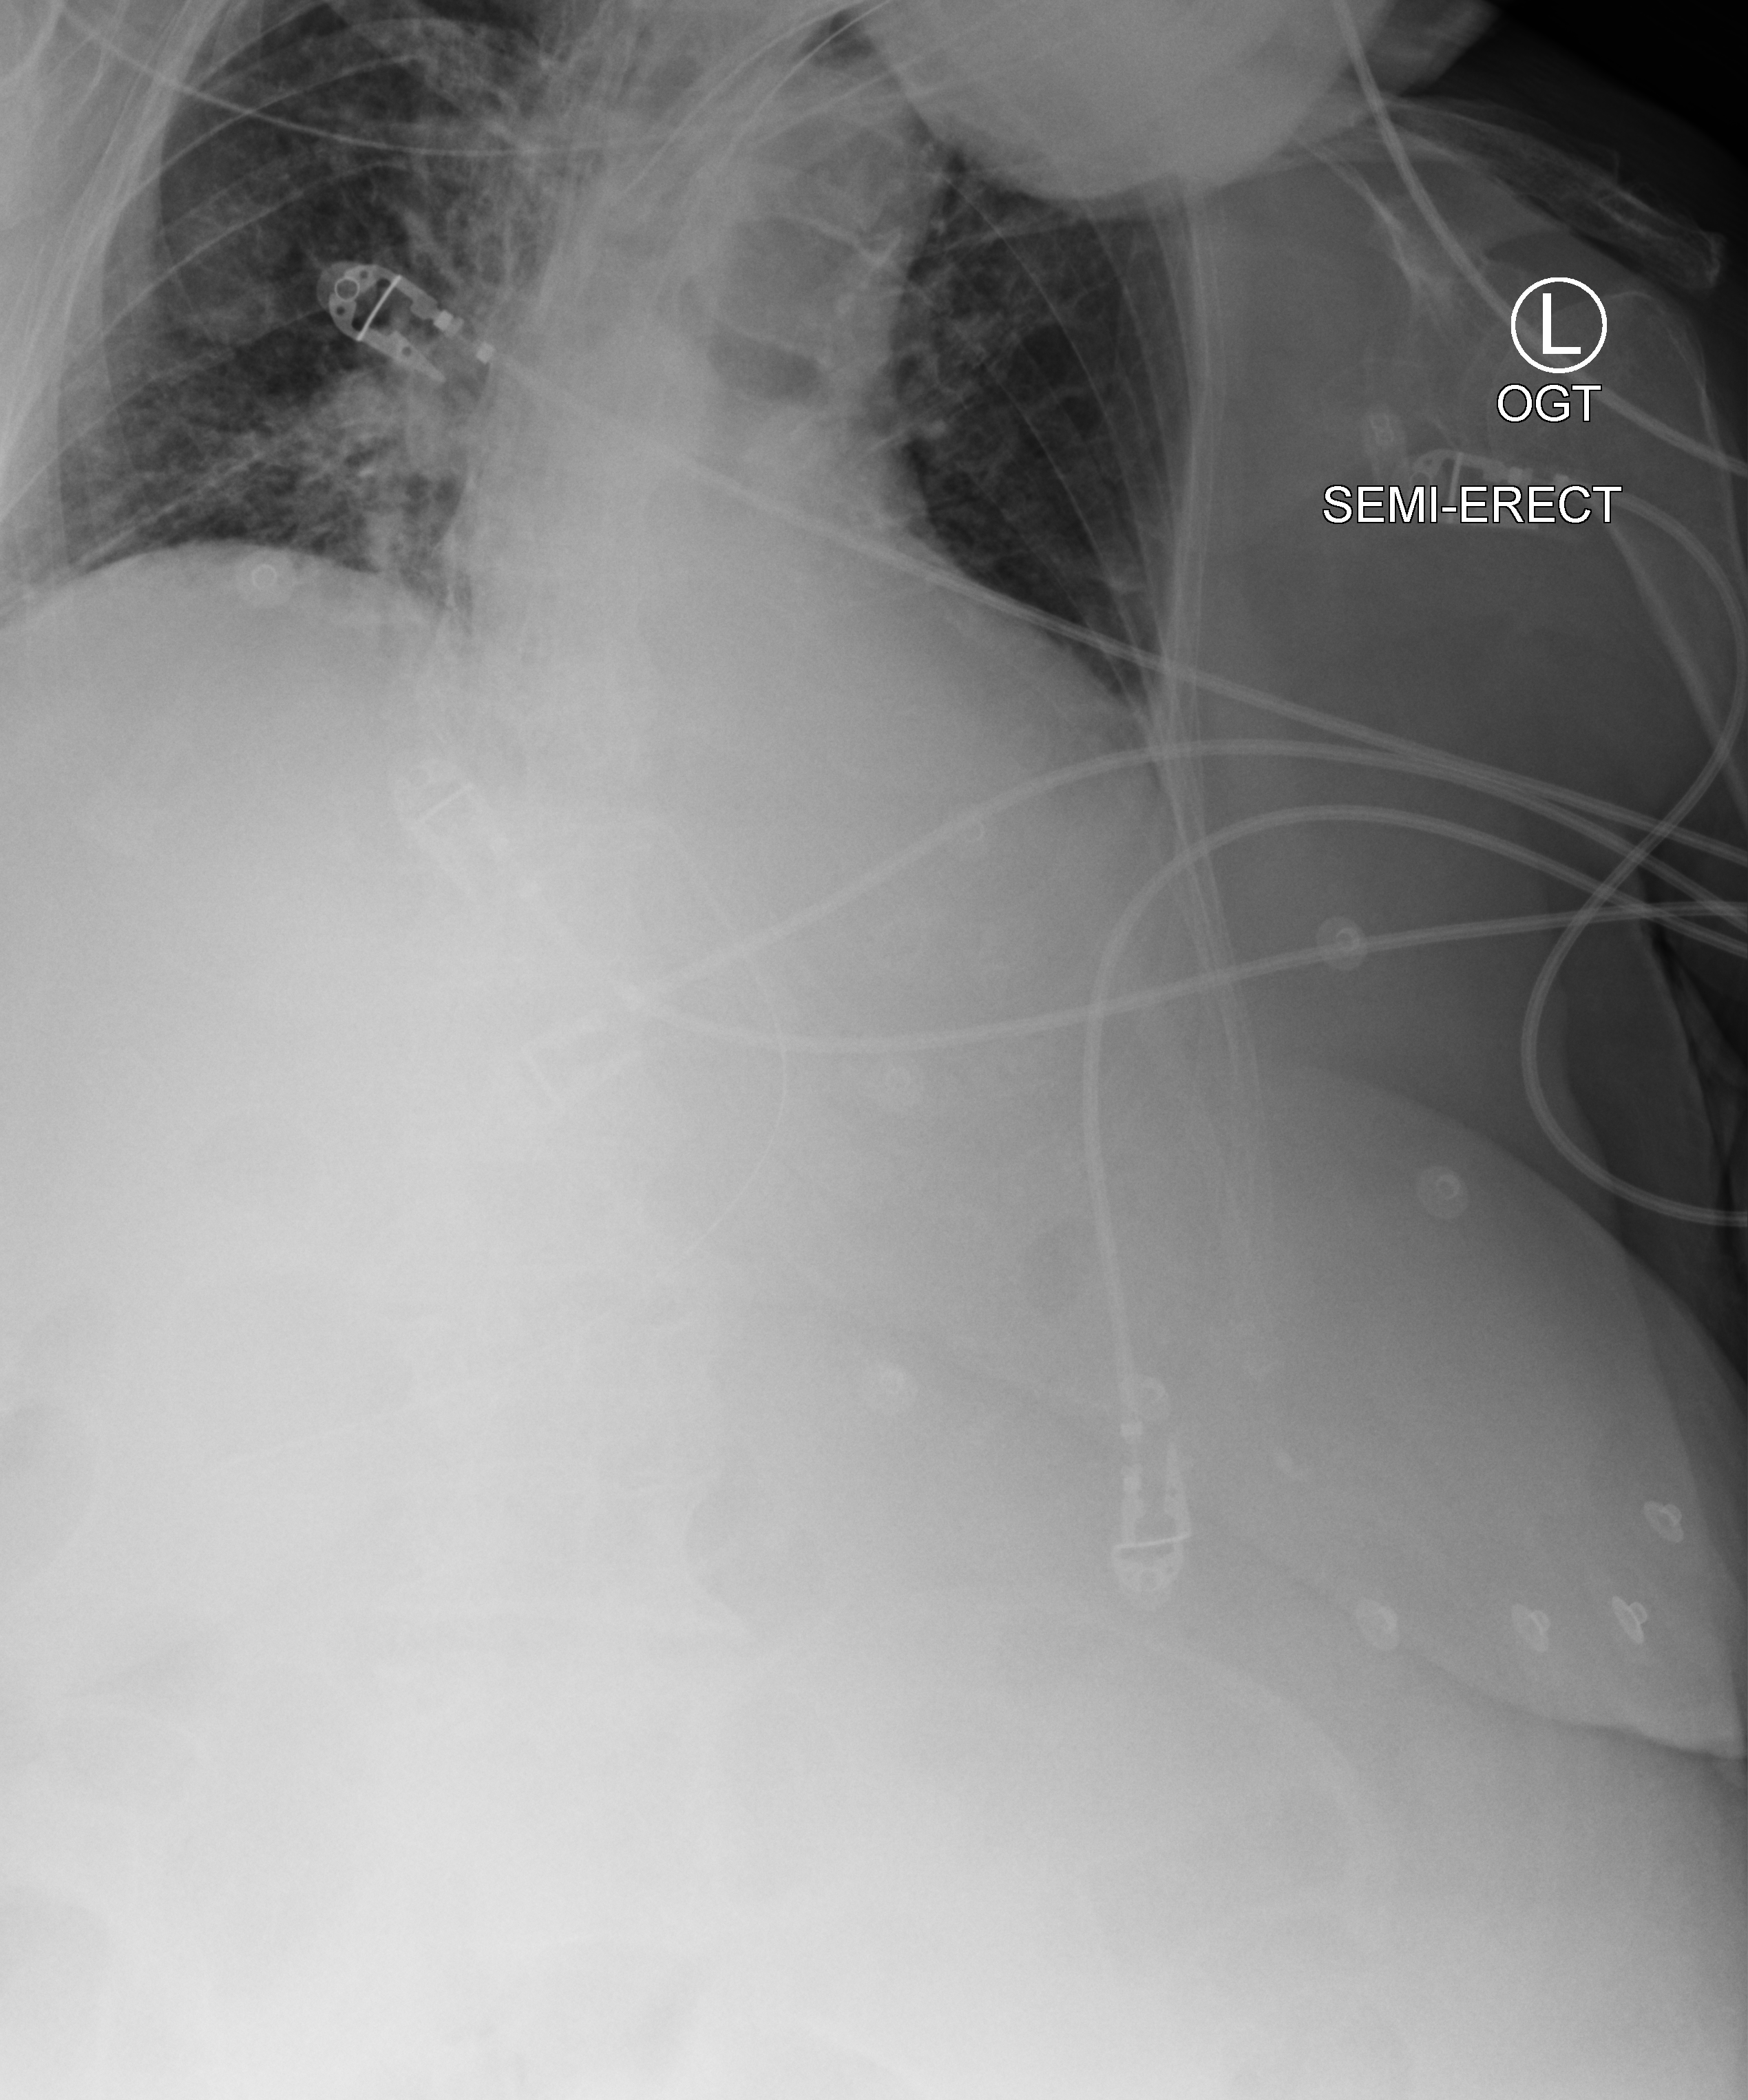
Bedside chest radiograph (computed radiography). Female patient hospitalised with COVID-19, age 75–90 years.
Hospital-stay facts (about this admission, not read from this image; timing relative to this image not recorded): other chronic lung disease (admission record): no; mechanically ventilated during this hospital stay: yes; hypertension (admission record): yes.